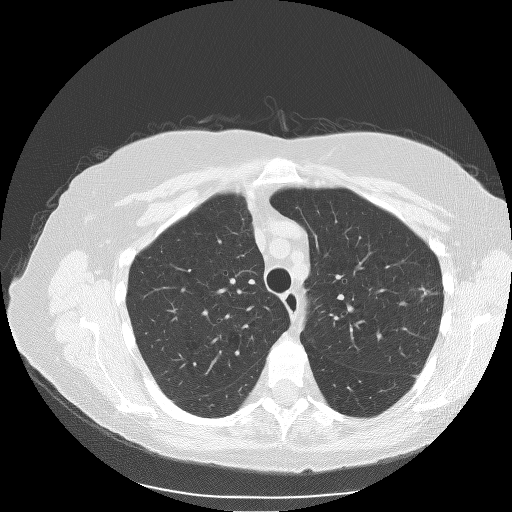
Axial slice from a low-dose chest CT screening exam. Baseline annual screen. Lung window (W 1500 / L -600 HU). Slice 72 of 106 in the series. 512 × 512 image matrix, field of view 360 × 360 mm. Female participant, aged 71 years at enrolment. Former smoker at enrolment.
- Expert-annotated lung lesion, bounding box <406,281,438,312> (left, top, right, bottom; pixels).
- Screening reader's record for this exam (one nodule recorded; not confirmed to be the boxed lesion): non-calcified nodule or mass ≥4 mm, left upper lobe, 15 × 9 mm, spiculated (stellate) margins, soft tissue attenuation.
- Official screen result: positive, change unspecified: nodule(s) >= 4 mm or enlarging nodule(s), mass(es), or other non-specific abnormalities suspicious for lung cancer.
- Later outcome: lung cancer diagnosed 77 days after this screen — adenocarcinoma, NOS, left upper lobe, moderately differentiated (G2), stage IA (AJCC 6th edition), 15 mm at pathology.